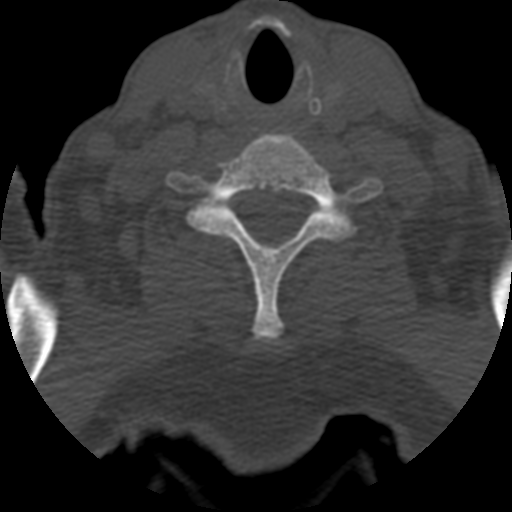
CT including the spine, one axial slice; position 530 of 708 along the scan axis; reconstruction kernel STANDARD; one of 3 acquisitions stored at this slice position; bone window (W 1800 / L 400 HU); 1.25 mm slice thickness; 512 × 512 image matrix, field of view 160 × 160 mm. Patient age 55 years. Case-level facts recorded for this patient, not image findings: primary cancer: colon; vertebrae with lytic lesions (as recorded): T12, L1, L5.
Structures marked on this image (semi-automatically segmented with operator editing):
- T1 vertebra: box from (x=187, y=200) to (x=356, y=236) px